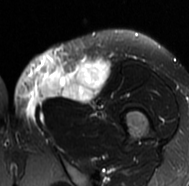
MRI of an extremity soft-tissue mass, one axial slice. Slice 29 of 77 in the series (ordered by position). T2-weighted fat-saturated. MR volume resampled by the dataset authors to the PET/CT grid (not the native acquisition matrix). 3.27 mm slice thickness. 189 × 186 image matrix, field of view 185 × 182 mm. Female patient. From the clinical record (not read from this slice): histological type: leiomyosarcoma; grade: high; site of the primary tumour: groin.
Annotated regions visible in this slice (expert contour drawn on MRI and transferred to this co-registered scan by the dataset authors):
- gross tumour volume including surrounding oedema: bounding box [x1, y1, x2, y2] px = [13, 50, 109, 126]
- gross tumour volume (mass): [38, 61, 109, 103]